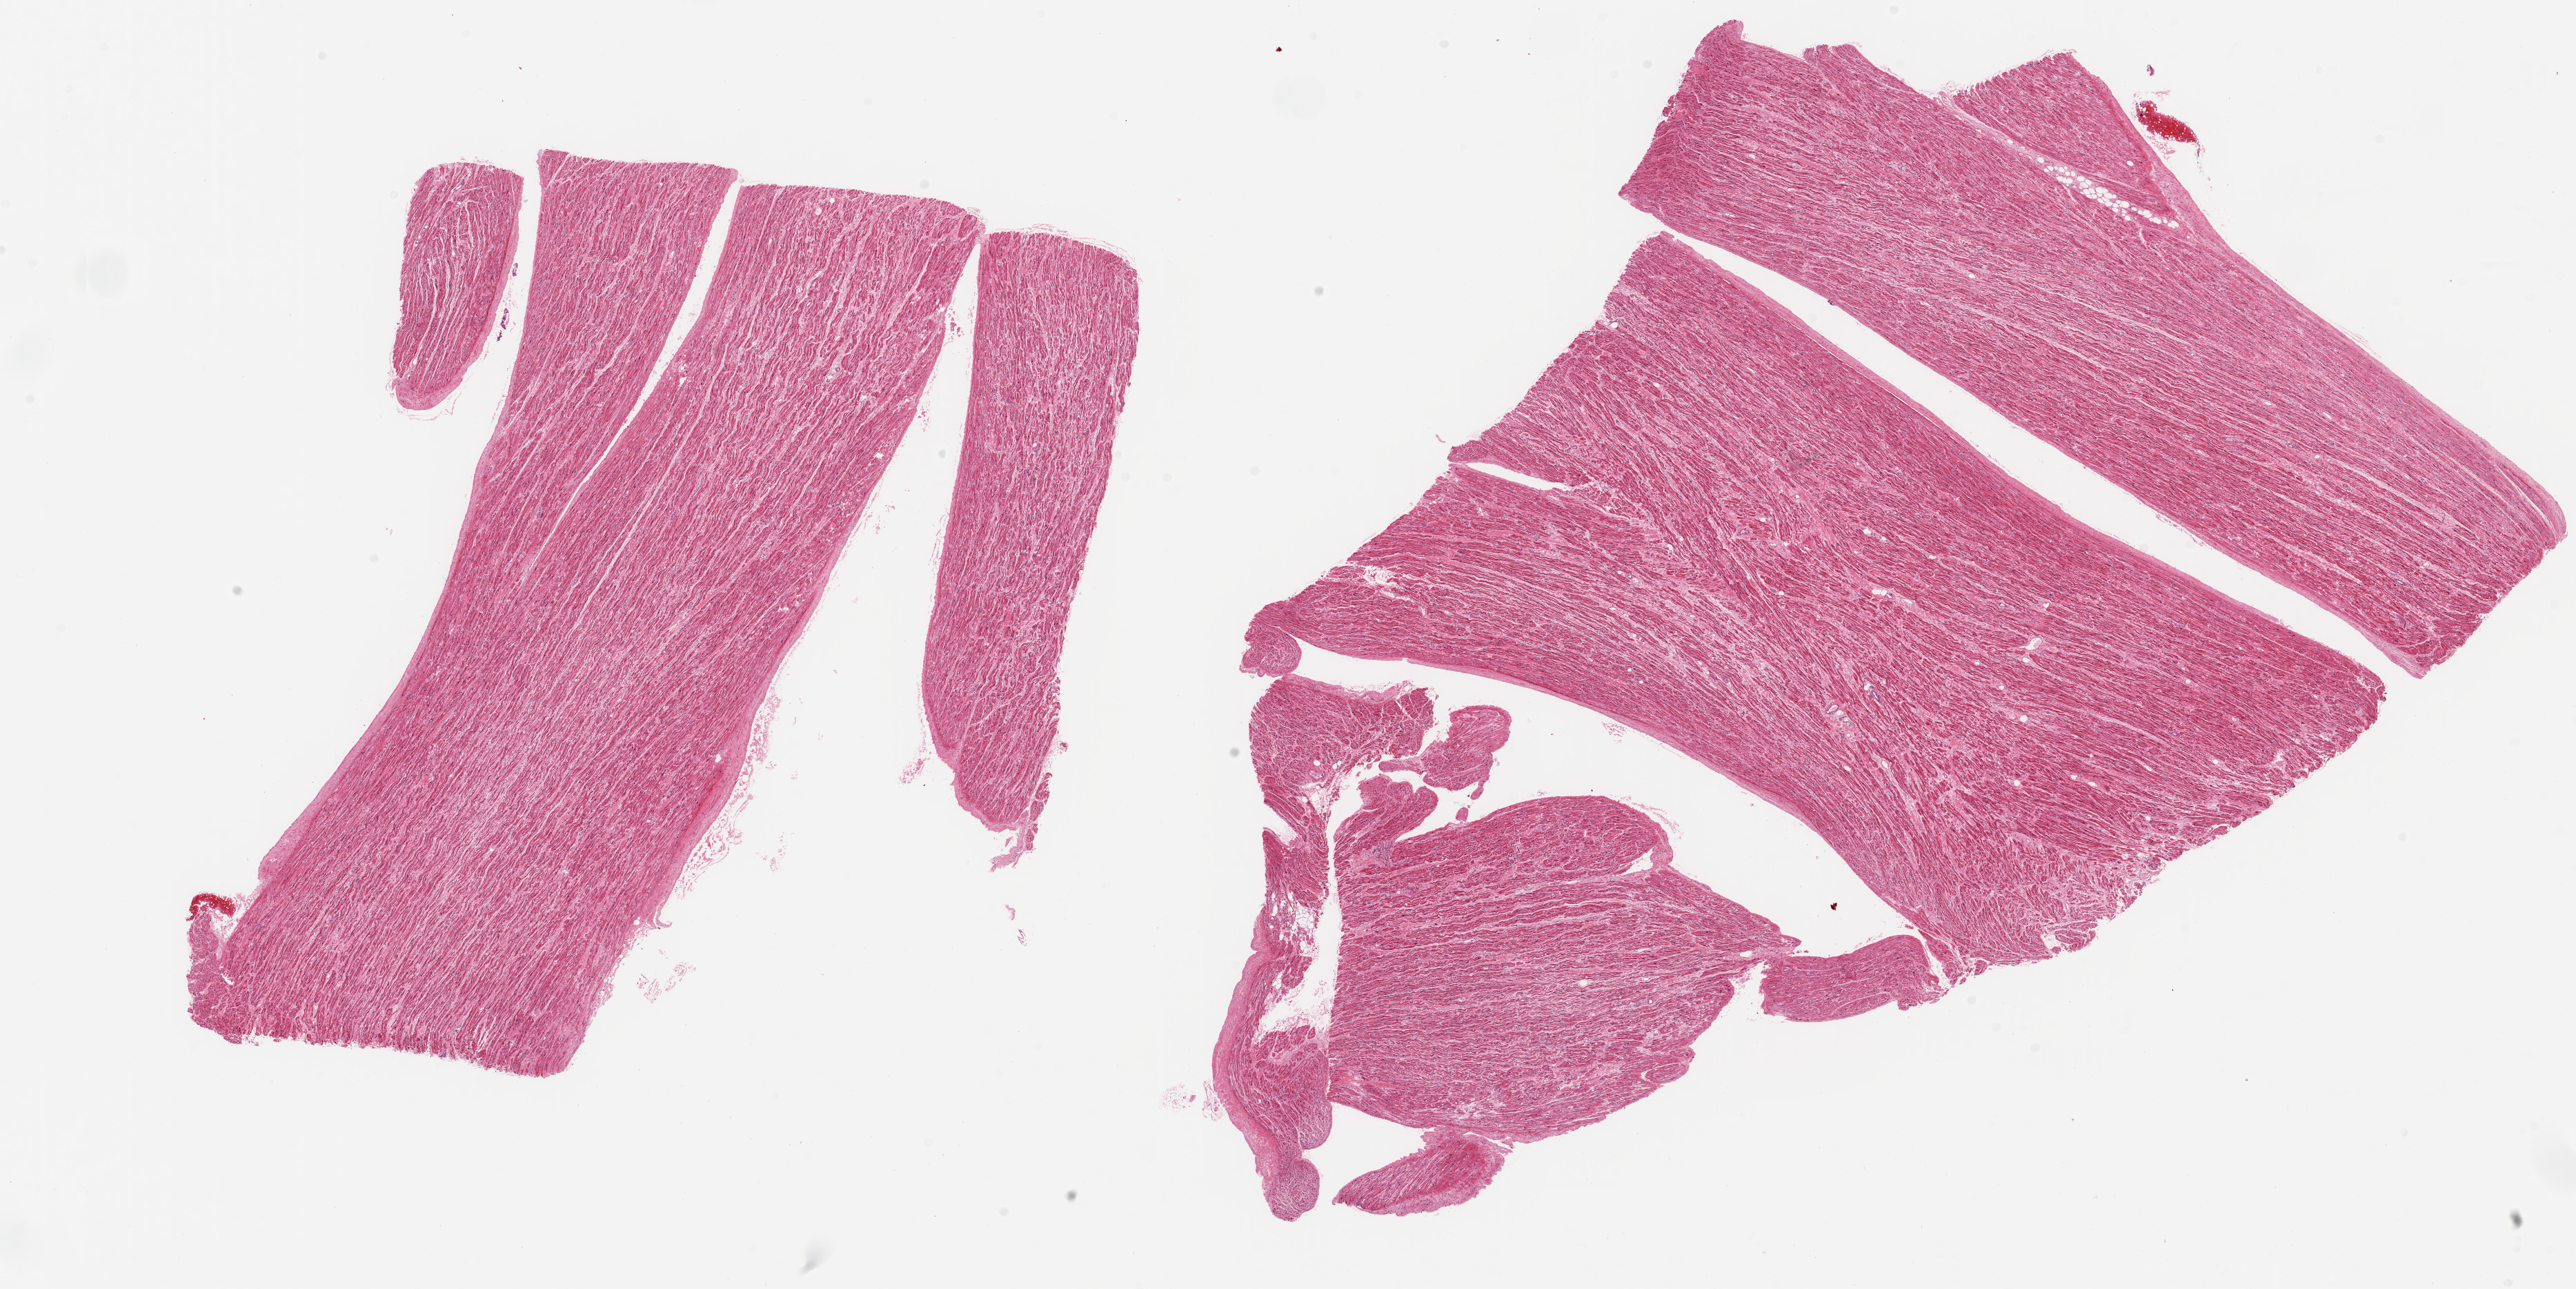
Digitized H&E-stained section, low-resolution overview of the scanned area, about 29.5 x 14.8 mm (acquisition: 20x scan). PAXgene-fixed paraffin-embedded (PFPE) section. Section of auricular appendage (target tissue). Donor tissue sample.
Review note (as recorded): 2 pieces, no abnormalities.